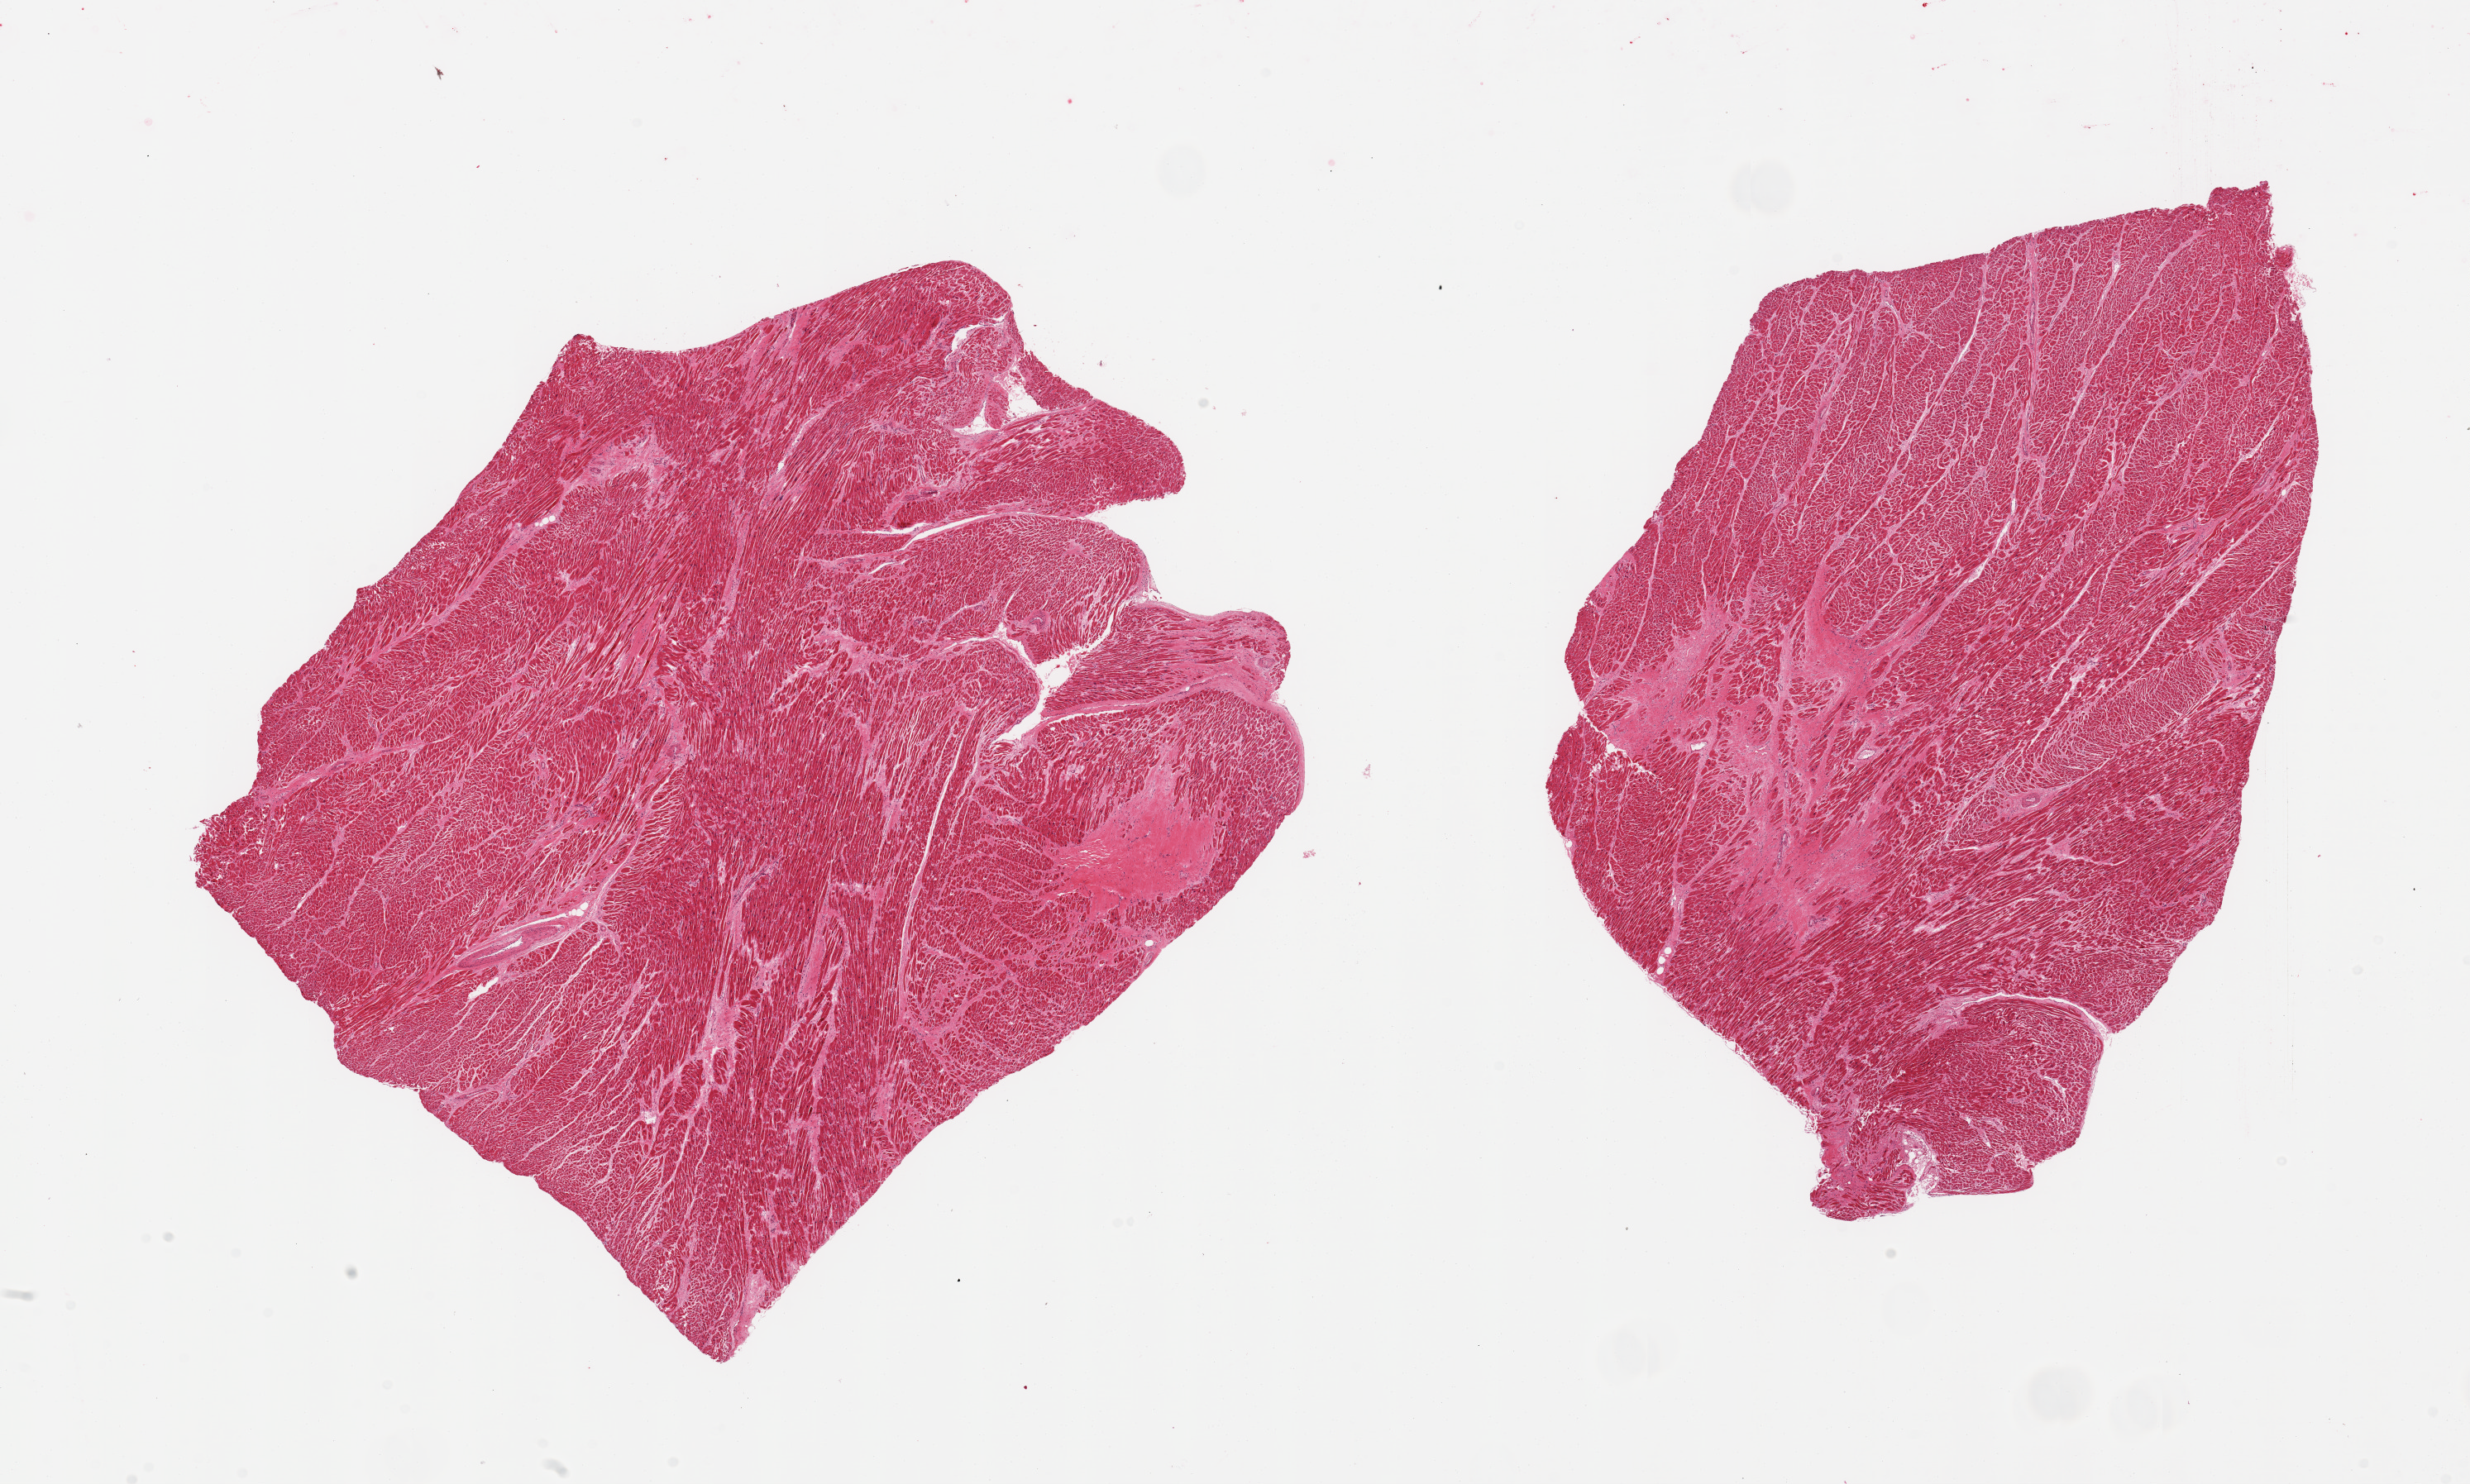
Whole-slide image, hematoxylin and eosin (H&E) stain — a low-resolution overview of the entire scanned area, about 23.6 x 14.2 mm (from a 20x scan), PAXgene-fixed paraffin-embedded (PFPE) section, sampled site (target tissue): heart, tissue donor sample. Donor sex: male.
Reviewer comment on this tissue sample: 2 pieces, marked chronic ischemic damage, remote infarcts, moderate-marked interstitial fibrosis.